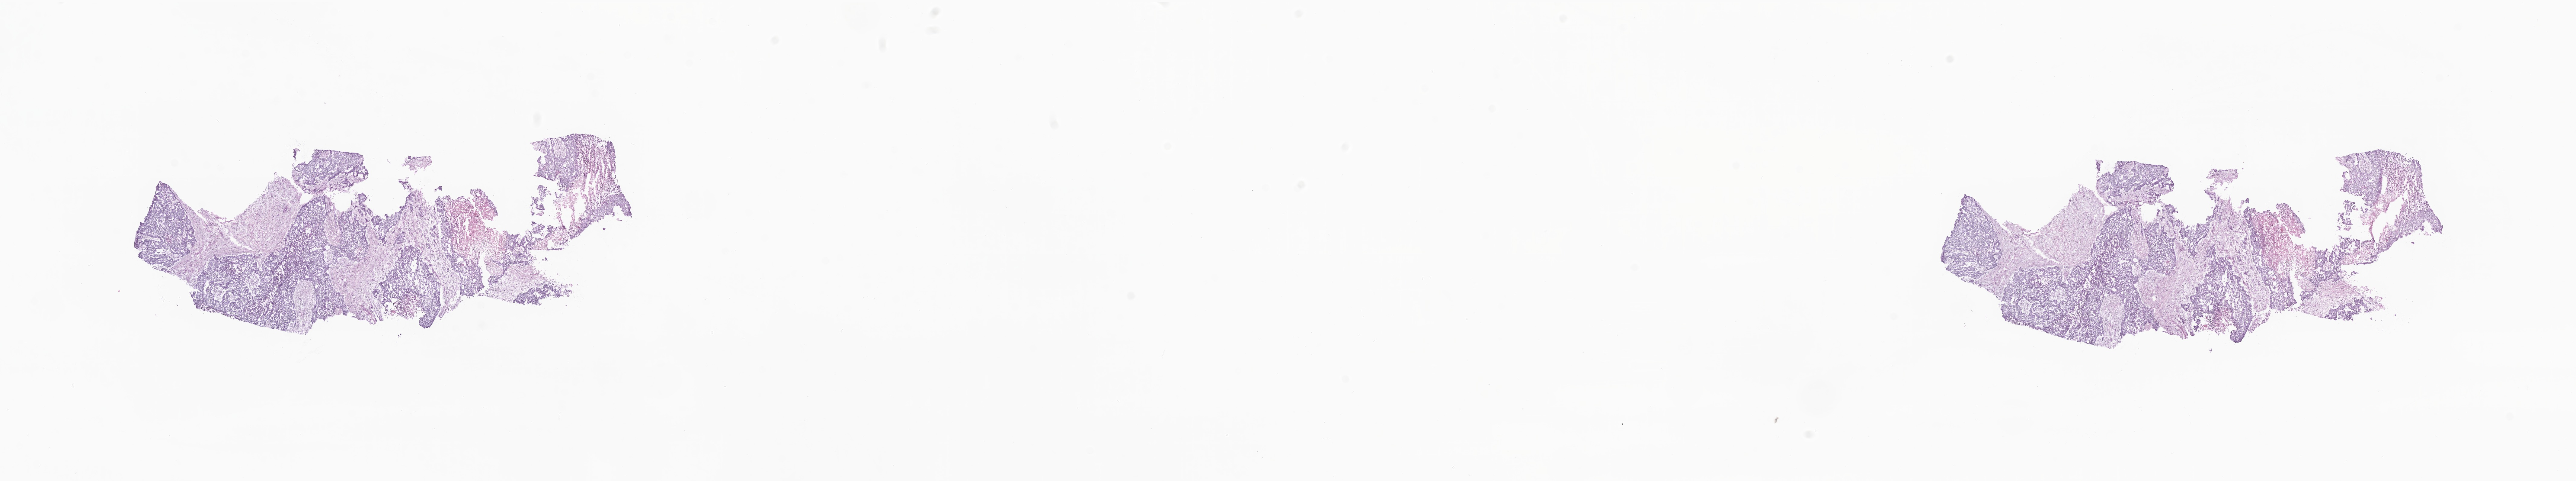
Digitized haematoxylin and eosin-stained section — shown as a low-resolution overview of the whole scanned area (about 36.0 x 6.7 mm); frozen section (tissue freezing medium); specimen: metastatic tumor tissue. Male patient; age at initial diagnosis 34 years. Pathologist review of this section (percent, as recorded): tumor cells 53%, tumor nuclei 87%, stromal cells 31%, necrosis 8%, normal cells 8%. Infiltration values recorded for this section: lymphocyte infiltration 1%, monocyte infiltration 0%, neutrophil infiltration 0%.
Patient diagnosis (primary): Adenocarcinoma, NOS. Section: top of the tissue portion.